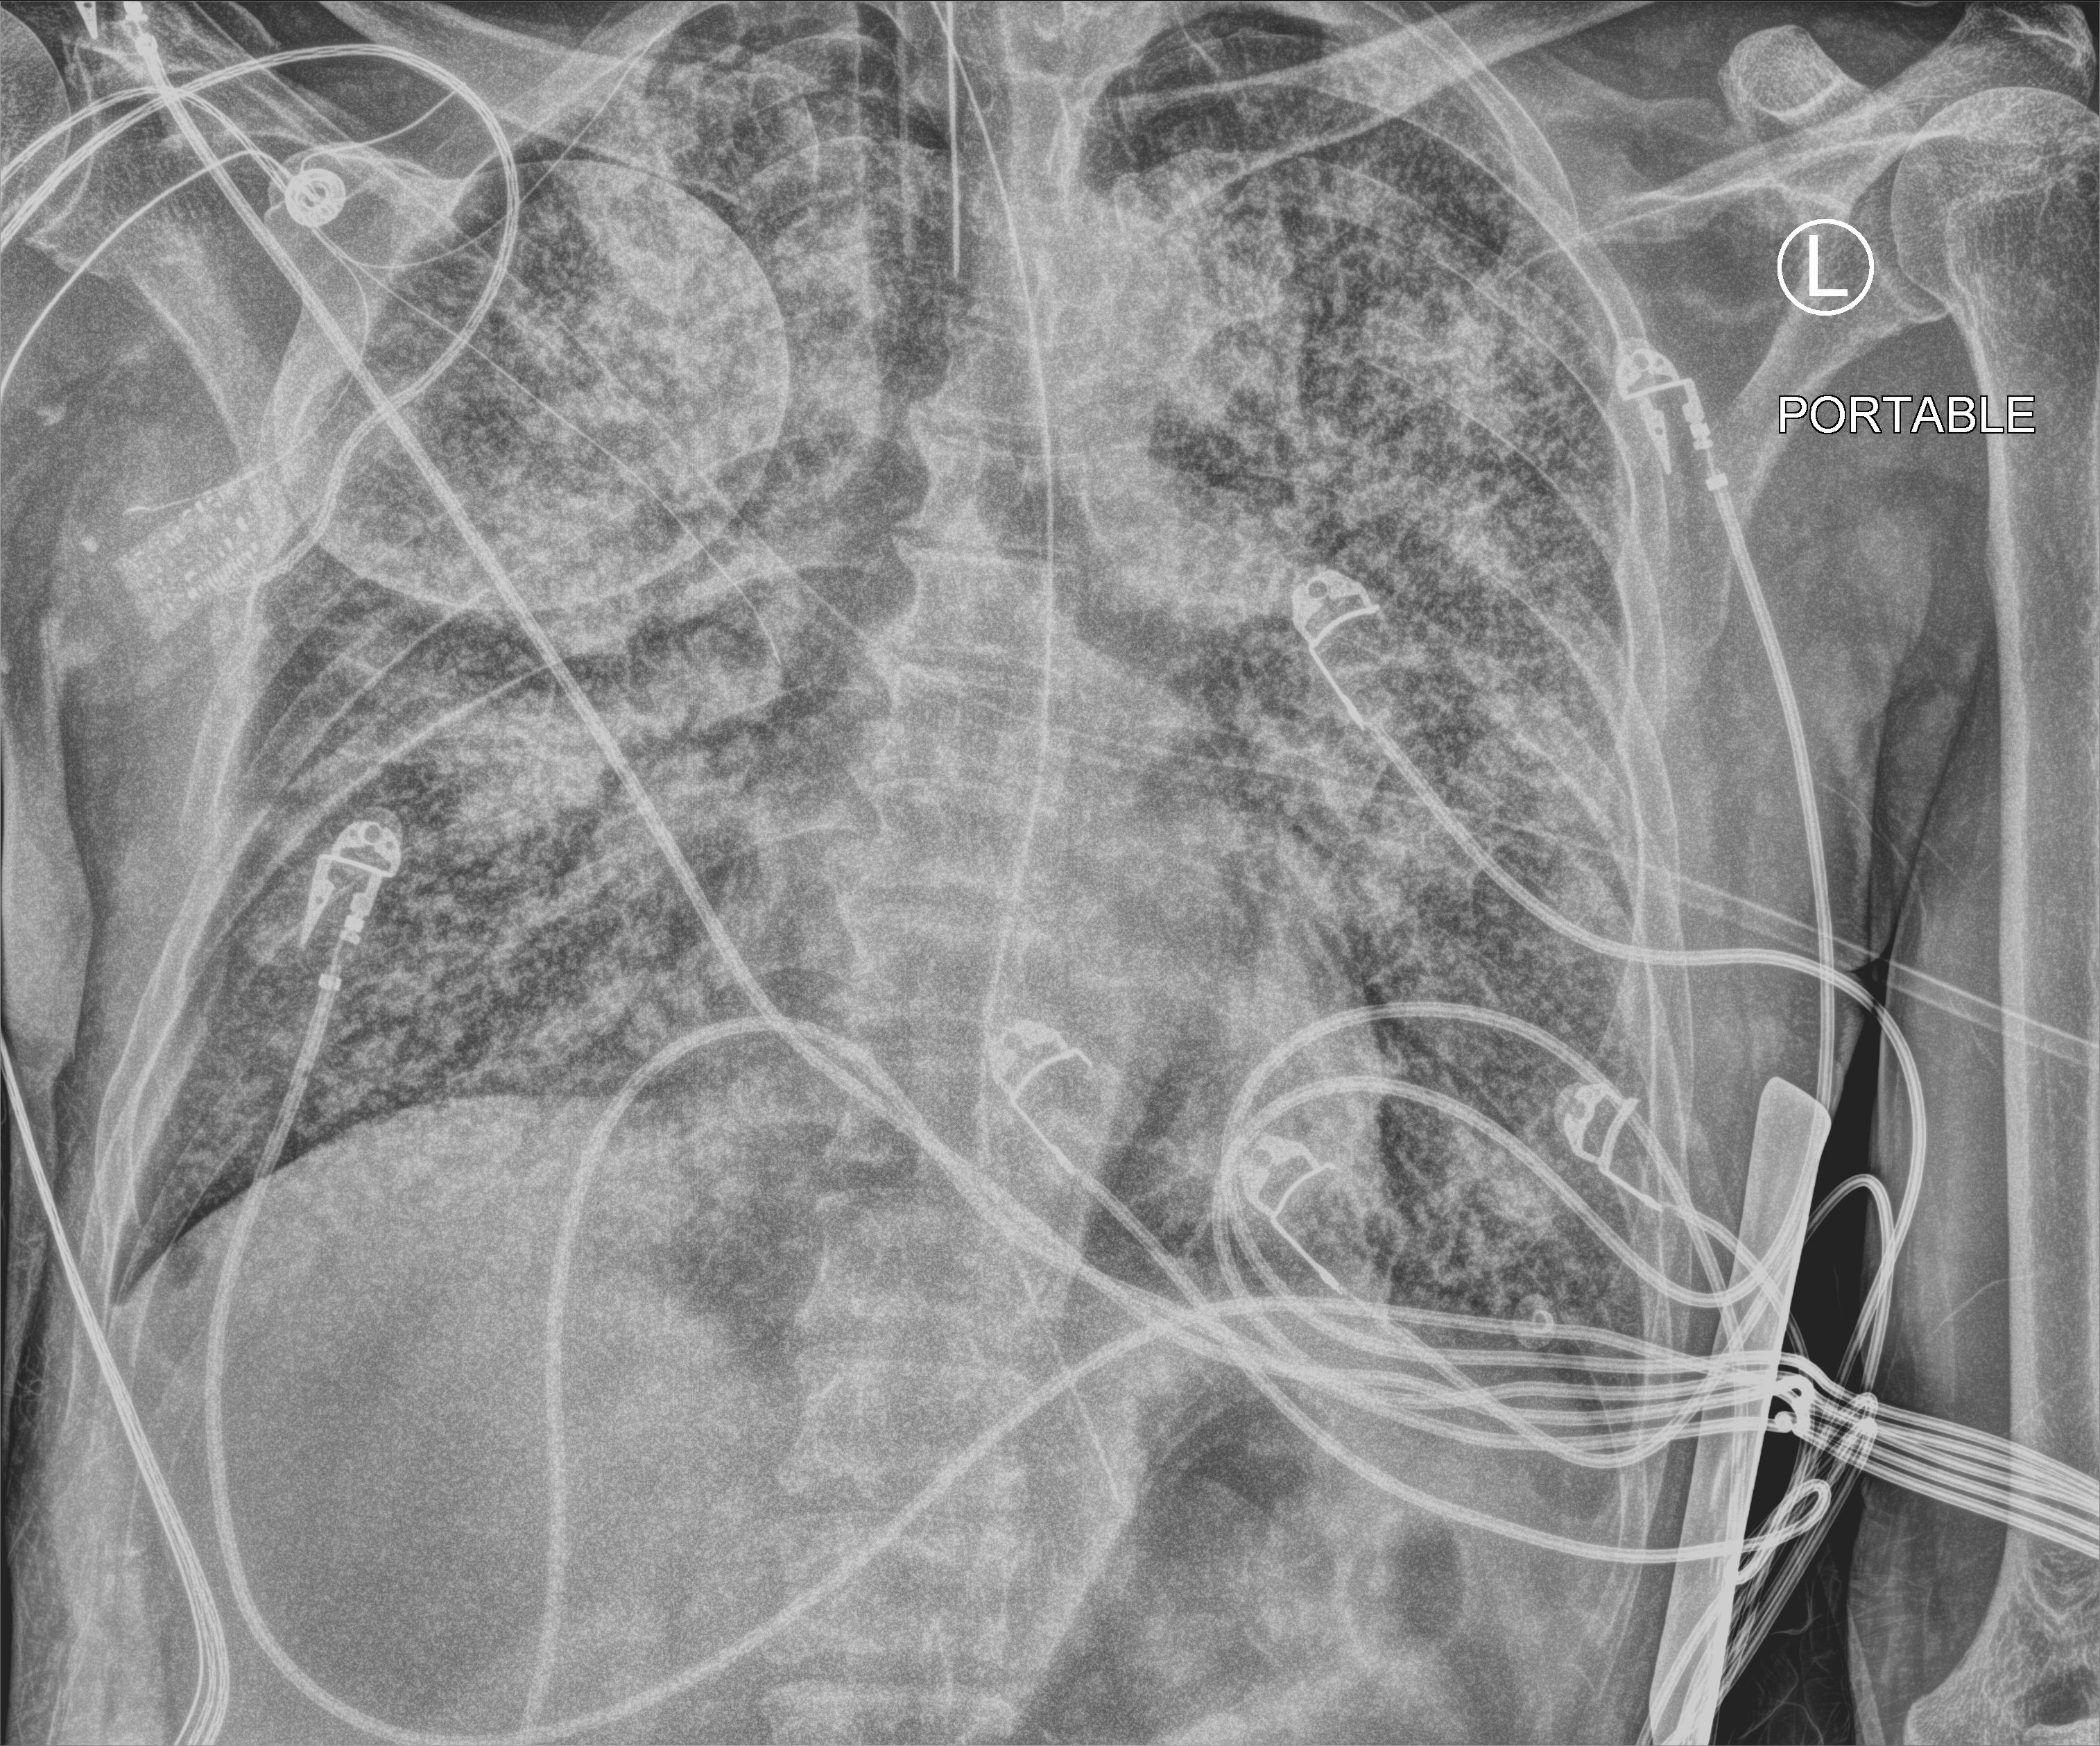
Portable chest radiograph, anteroposterior (AP) projection. Patient hospitalised with COVID-19; male, aged 60–74 years.
Admission-level facts for this patient (not findings on this image; timing relative to this image not recorded):
- admitted to intensive care during this hospital stay: yes
- other chronic lung disease (admission record): no